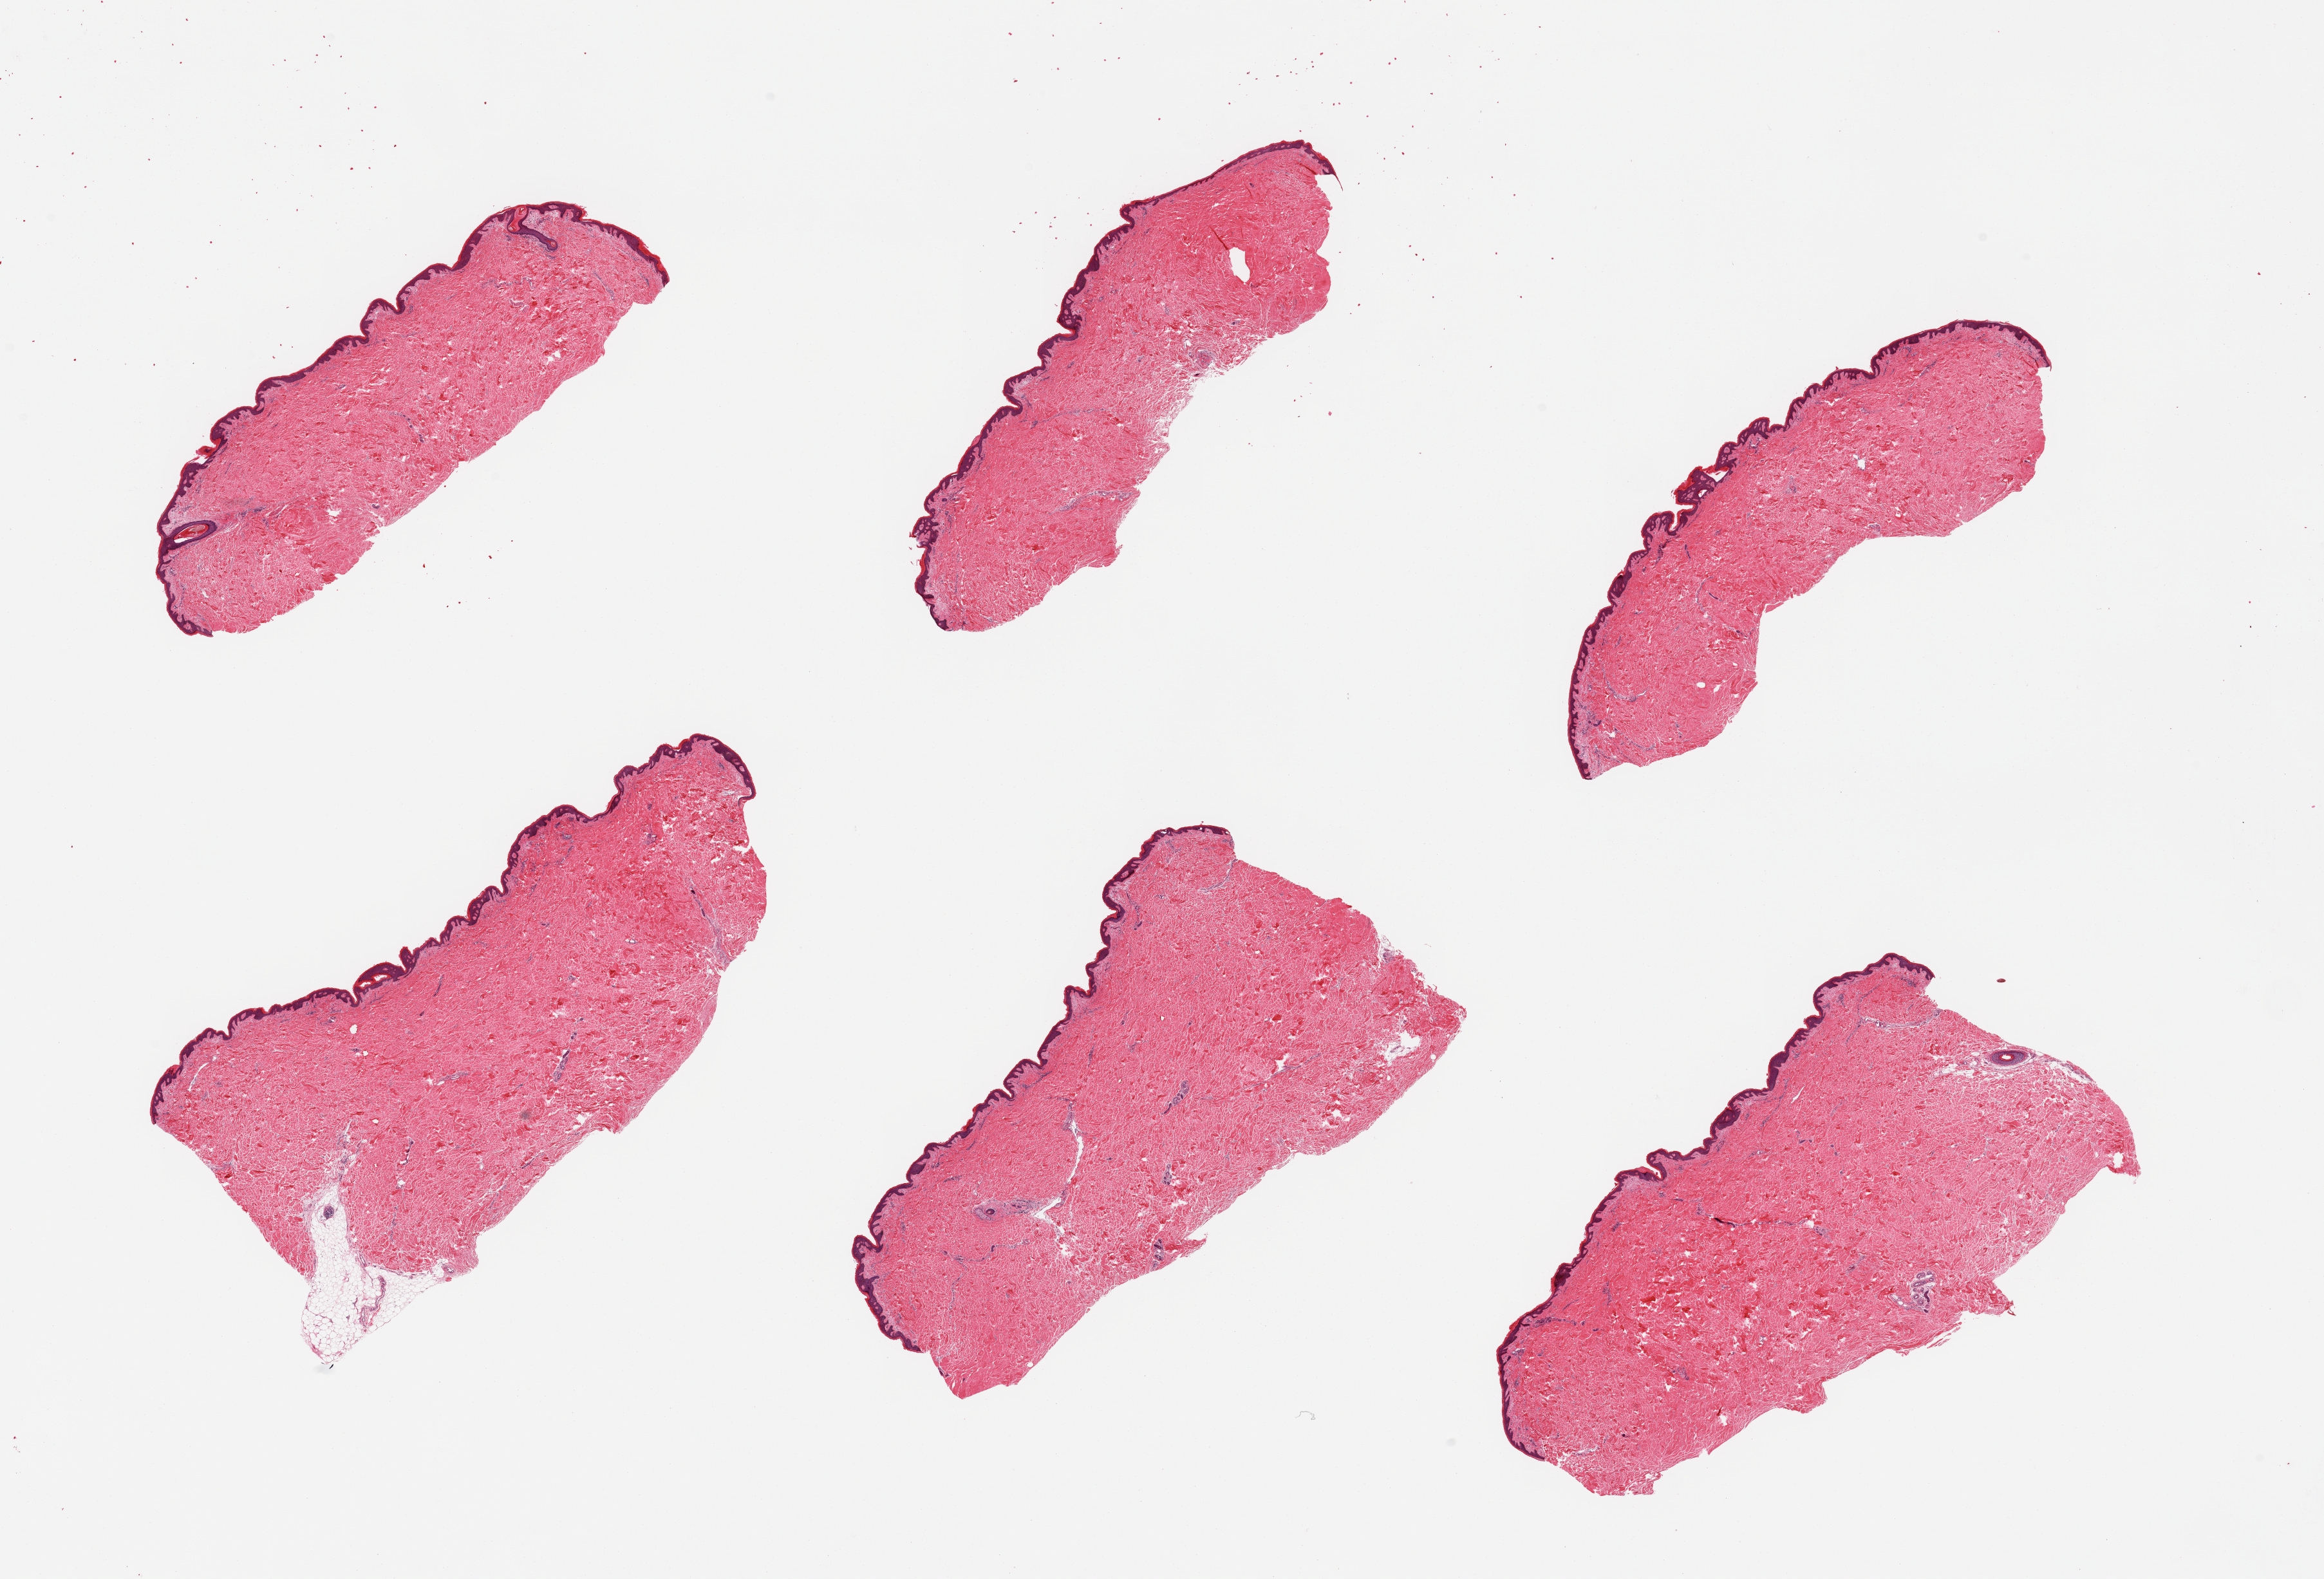
Whole-slide image, hematoxylin and eosin (H&E) stain, brightfield — shown as a low-resolution overview of the whole scanned area (about 28.5 x 19.4 mm, slide scanned at 20x), PAXgene-fixed, paraffin-embedded tissue, sampled site (target tissue): skin of suprapubic region, tissue donor sample.
* review note (as recorded): 6 pieces; well dissected; virtually fat free dermis